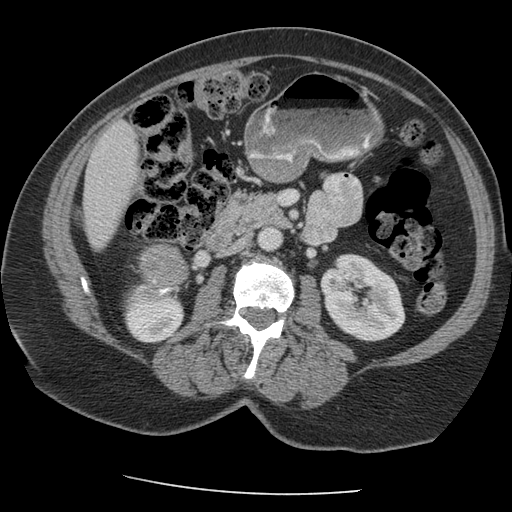
Contrast-enhanced abdominal CT, one axial slice; position 104 of 163 along the scan axis; reconstruction kernel STANDARD; intravenous contrast given; soft-tissue window (W 400 / L 40 HU); 2.5 mm slice thickness; 512 × 512 image matrix, field of view 360 × 360 mm. Patient: female, 70 years. Case-level facts recorded for this patient, not image findings: diagnosis: adrenocortical carcinoma; tumour side: right adrenal; tumour size at pathology: 9.5 cm; Ki-67 index: 5 %; stage (as recorded): 2.
Annotated regions visible in this slice (semi-automatic segmentation, software-assisted and operator-edited):
- mass: box from (x=140, y=245) to (x=186, y=284) px